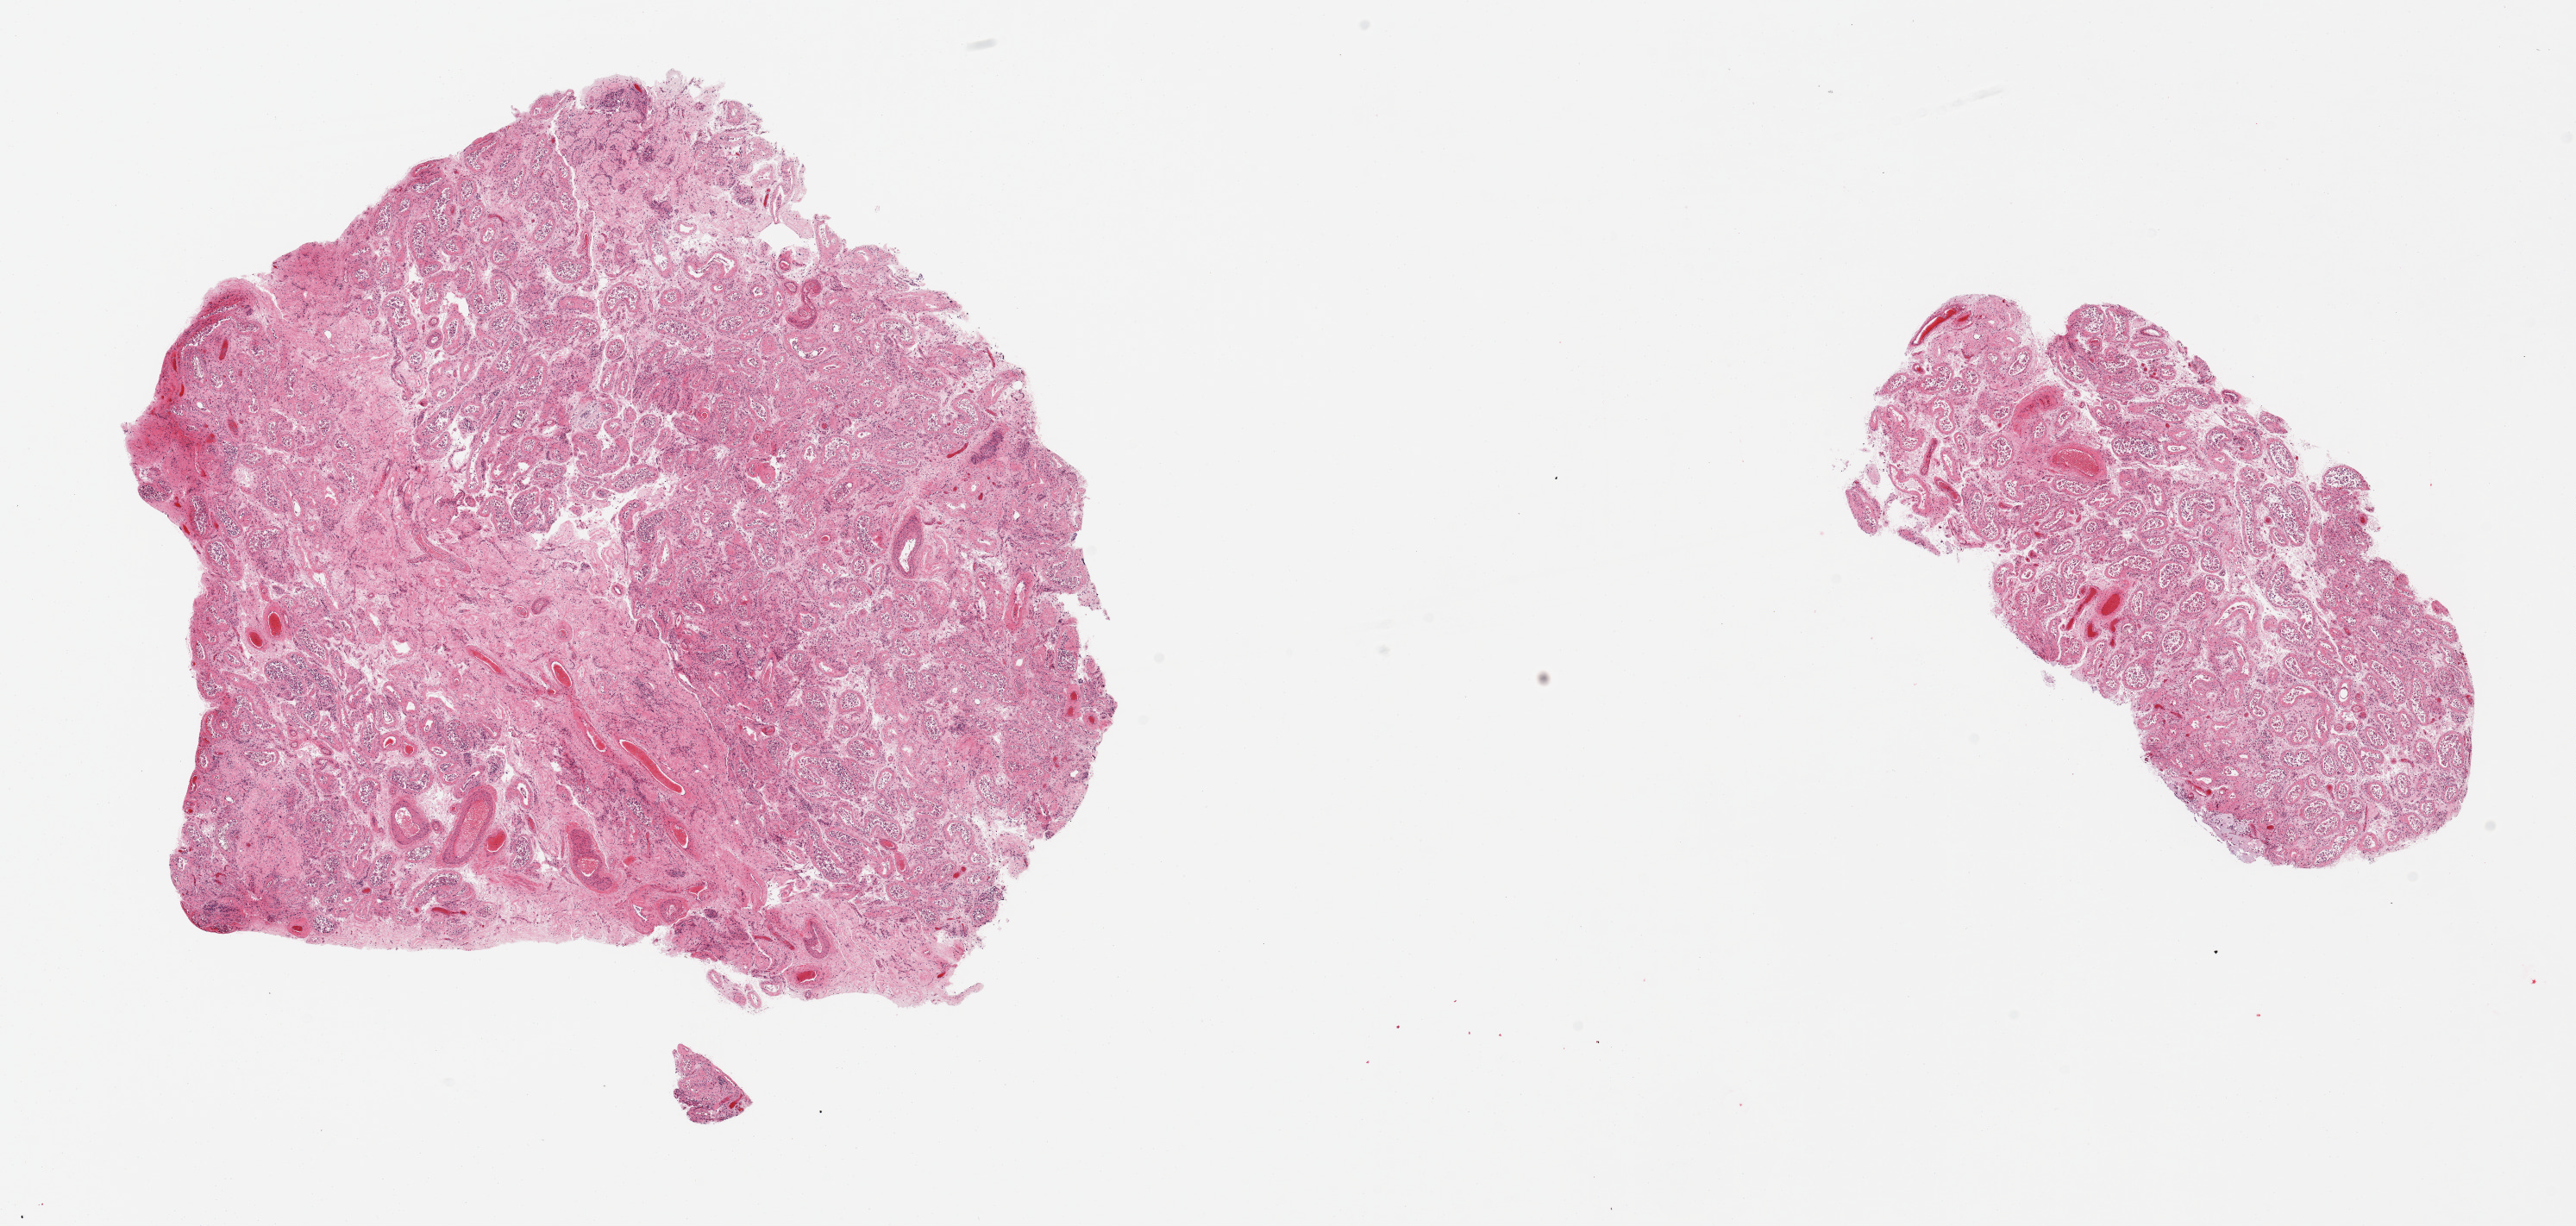
Haematoxylin and eosin whole-slide image, brightfield — low-resolution overview of the scanned area, about 23.6 x 11.2 mm (slide scanned at 20x), PAXgene-fixed paraffin-embedded (PFPE) section, section of testis (target tissue), donor tissue sample. Donor sex: male.
Review note (as recorded): 2 pieces, marked tubular atrophy.